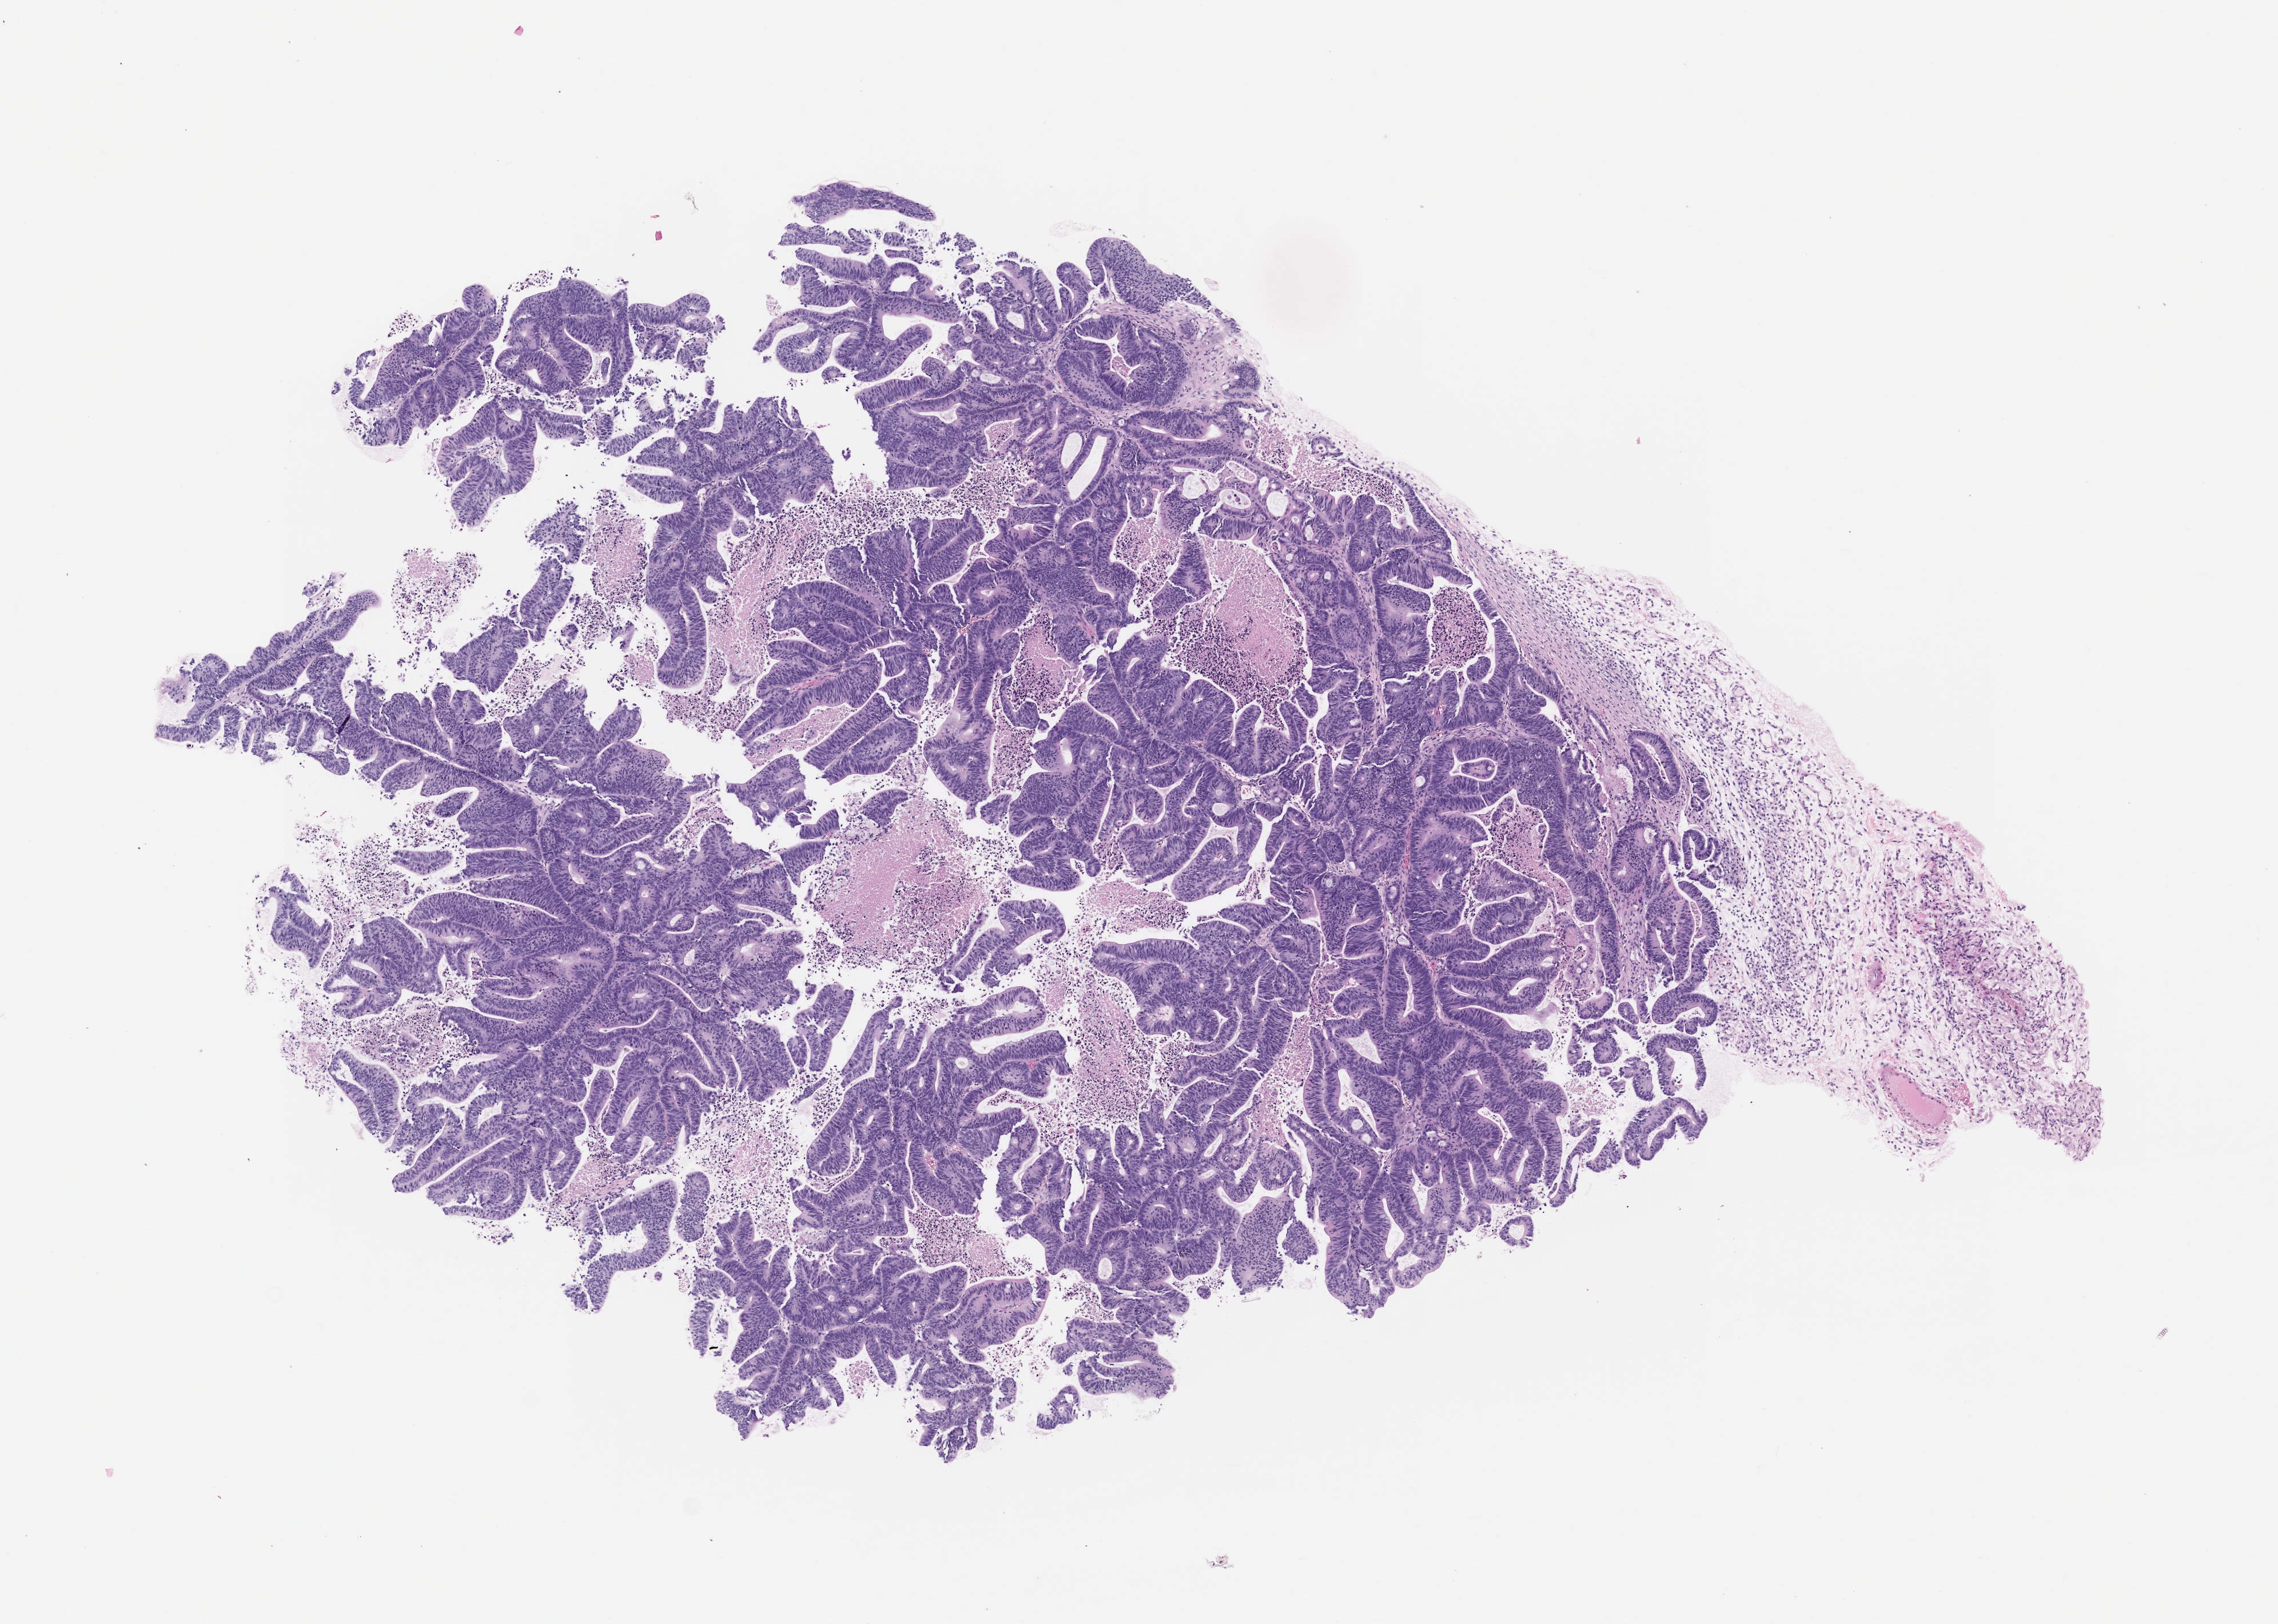
H&E whole-slide image of a patient-derived xenograft (PDX) tumor grown in a mouse, passage 0, whole scanned area (about 8.0 x 5.7 mm) shown as a low-resolution overview, formalin-fixed paraffin-embedded section, tumor site category: colon.
* originating patient diagnosis: Colon Adenocarcinoma